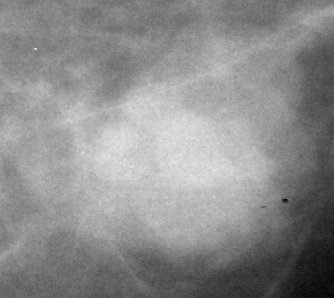
Crop from a digitized film mammogram around one marked abnormality; left breast; CC view.
- Mass, shape lobulated, margins microlobulated; BI-RADS assessment category 5; pathology result (as recorded, not read from the image): malignant.